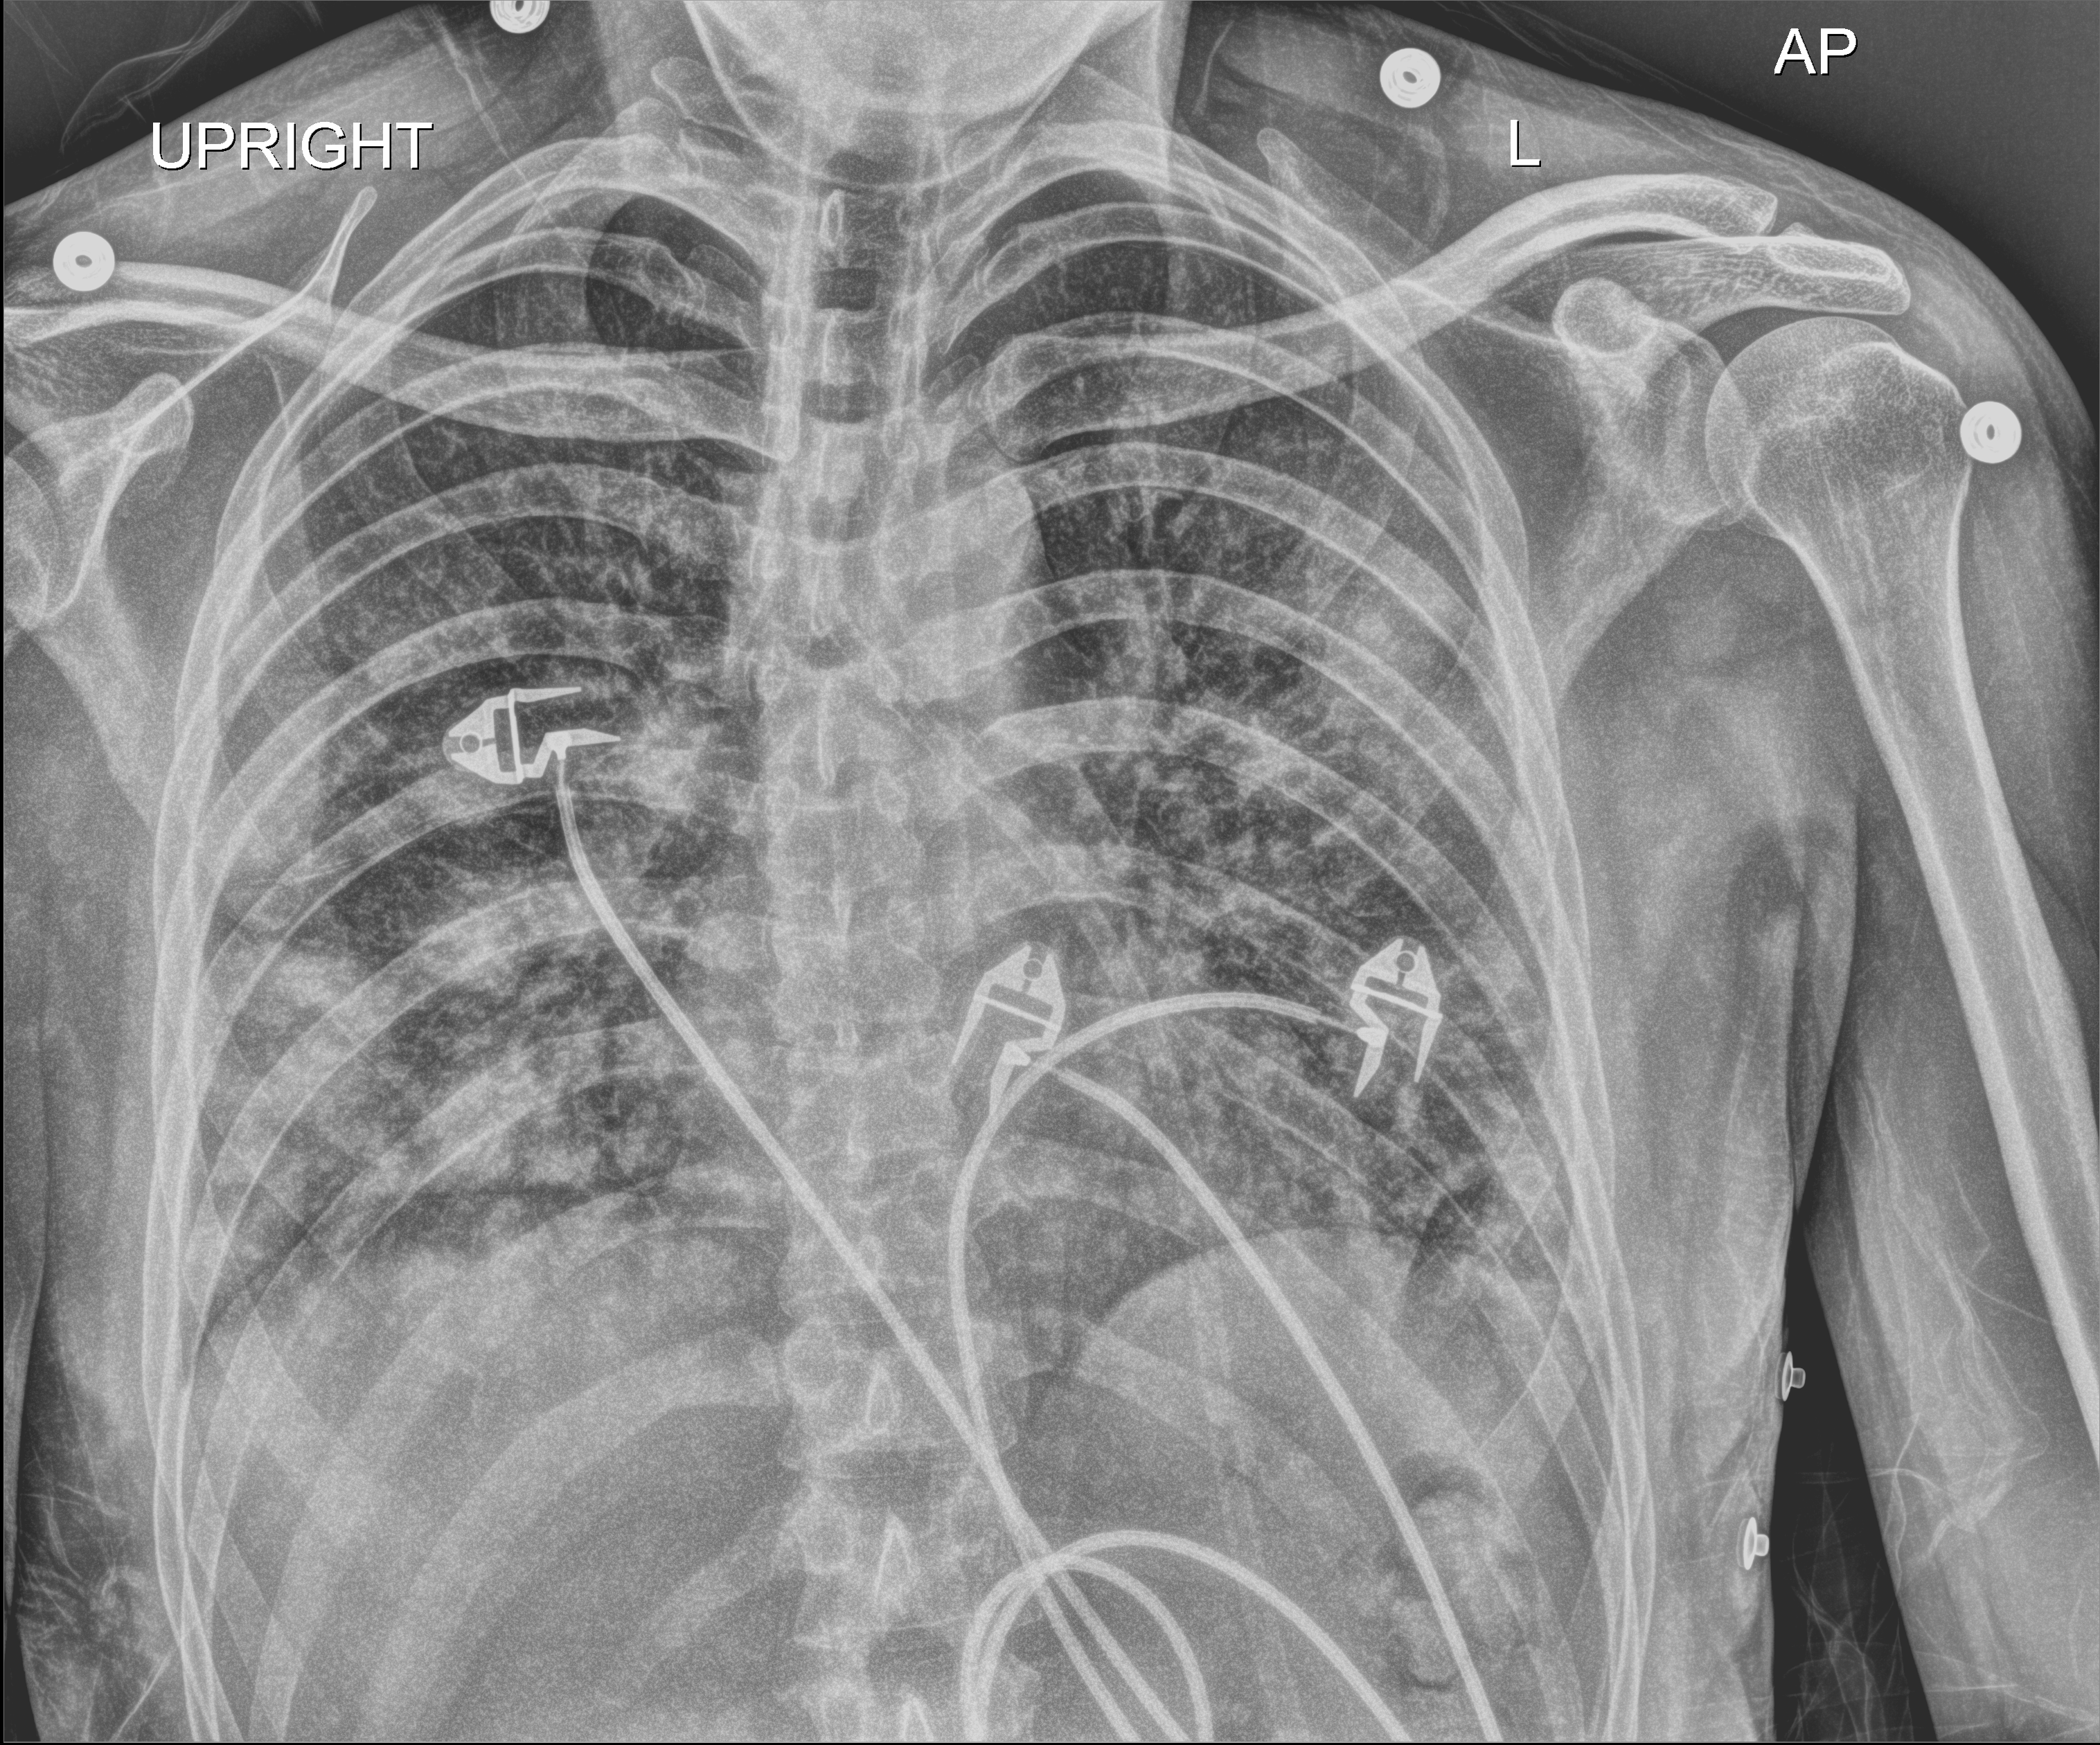
Bedside chest radiograph (digital radiography); anteroposterior (AP) projection. Patient hospitalised with COVID-19; male, aged 18–59 years.
Hospital-stay facts (about this admission, not read from this image; timing relative to this image not recorded): diabetes (admission record): no; admitted to intensive care during this hospital stay: no.